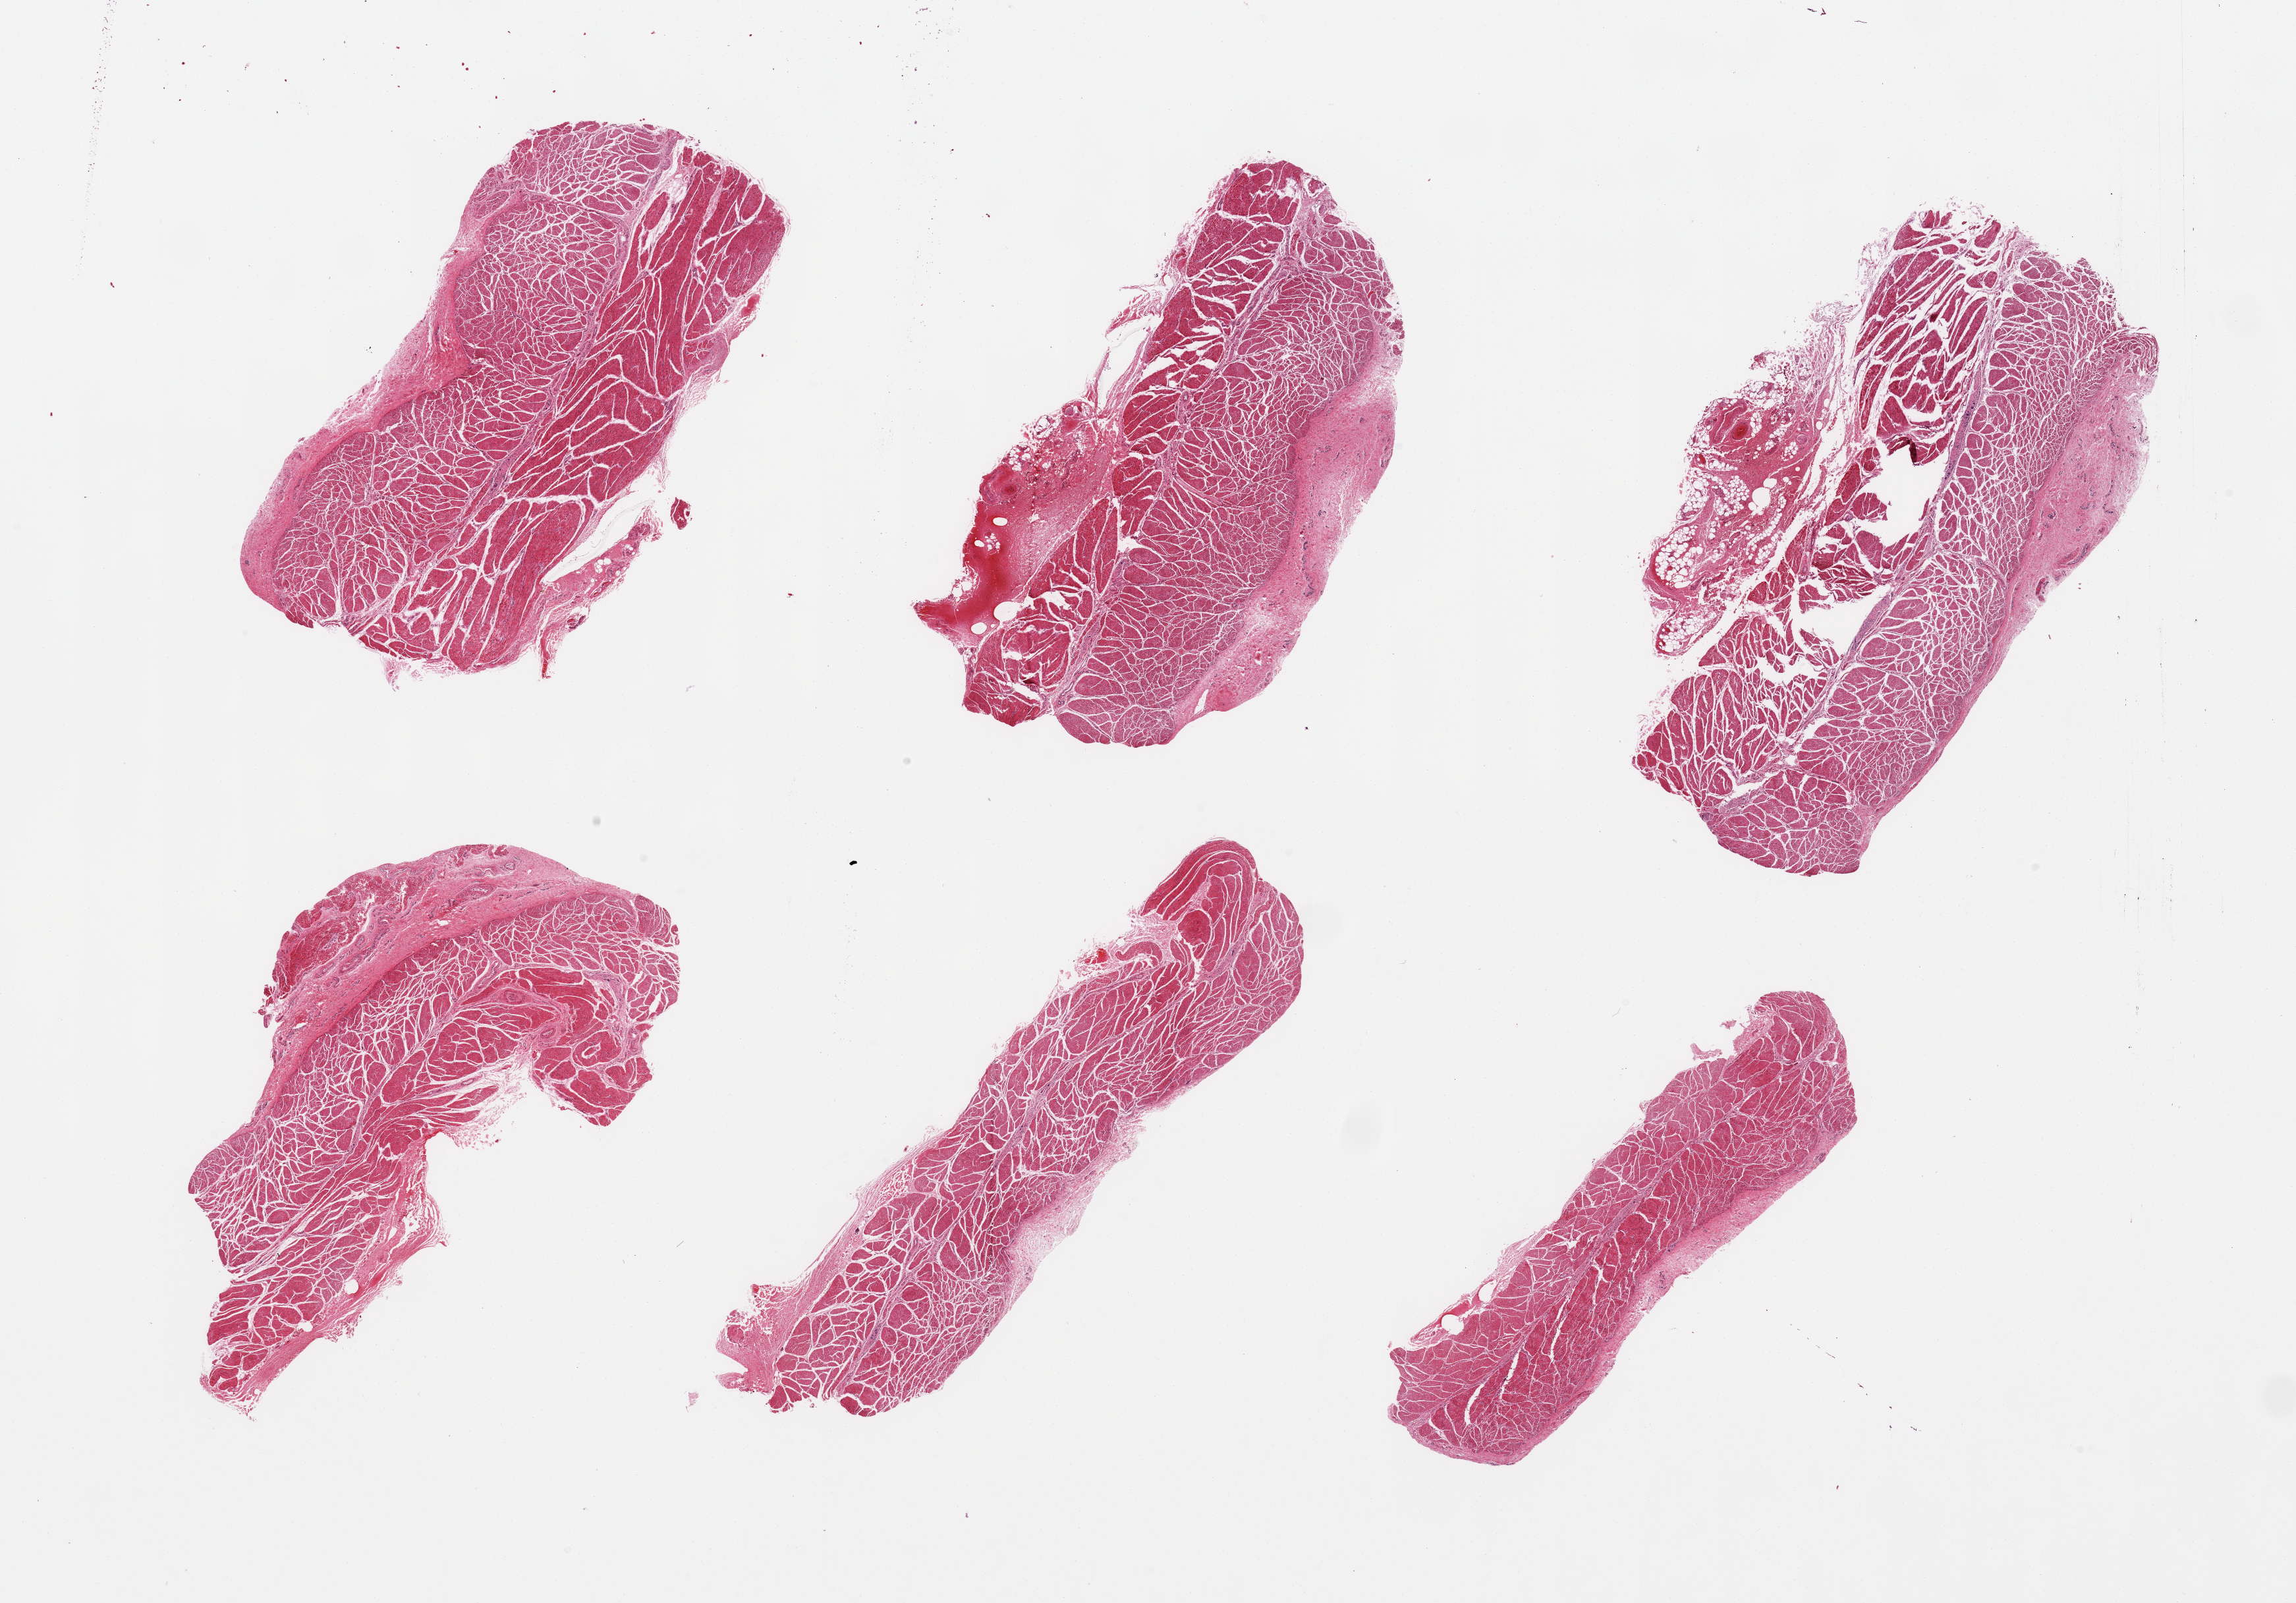
Hematoxylin and eosin (H&E) whole-slide image, whole scanned area (about 27.6 x 19.2 mm) shown as a low-resolution overview, PAXgene-fixed paraffin-embedded (PFPE) section, target tissue: esophageal muscle, donor tissue sample. Donor: male.
Pathologist's review note for this sample: 6 pieces; up to 20% external fibrofatty content.